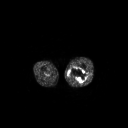
FDG PET of an extremity soft-tissue mass (from a PET/CT study), one axial slice. Slice 218 of 267 in the series (ordered by position). 3.27 mm slice thickness. 128 × 128 image matrix, field of view 700 × 700 mm. Patient: male, 44 years. Case-level facts recorded for this patient, not image findings: histological type: undifferentiated pleomorphic liposarcoma; grade: high; site of the primary tumour: left thigh.
Structures marked on this image (expert contour drawn on MRI and transferred to this co-registered scan by the dataset authors):
- gross tumour volume including surrounding oedema: box from (x=68, y=67) to (x=87, y=83) px
- gross tumour volume (mass): (x=68, y=67)–(x=87, y=83)